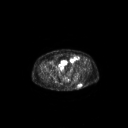
FDG PET of an extremity soft-tissue mass (from a PET/CT study), one axial slice. Position 72 of 267 along the scan axis. 128 × 128 image matrix, field of view 700 × 700 mm. Male patient, age 69 years. From the clinical record (not read from this slice): histological type: leiomyosarcoma; grade: intermediate; site of the primary tumour: left pelvis.
Outlined on this slice (expert contour drawn on MRI and transferred to this co-registered scan by the dataset authors):
- gross tumour volume (mass): bounding box [x1, y1, x2, y2] px = [78, 84, 82, 87]